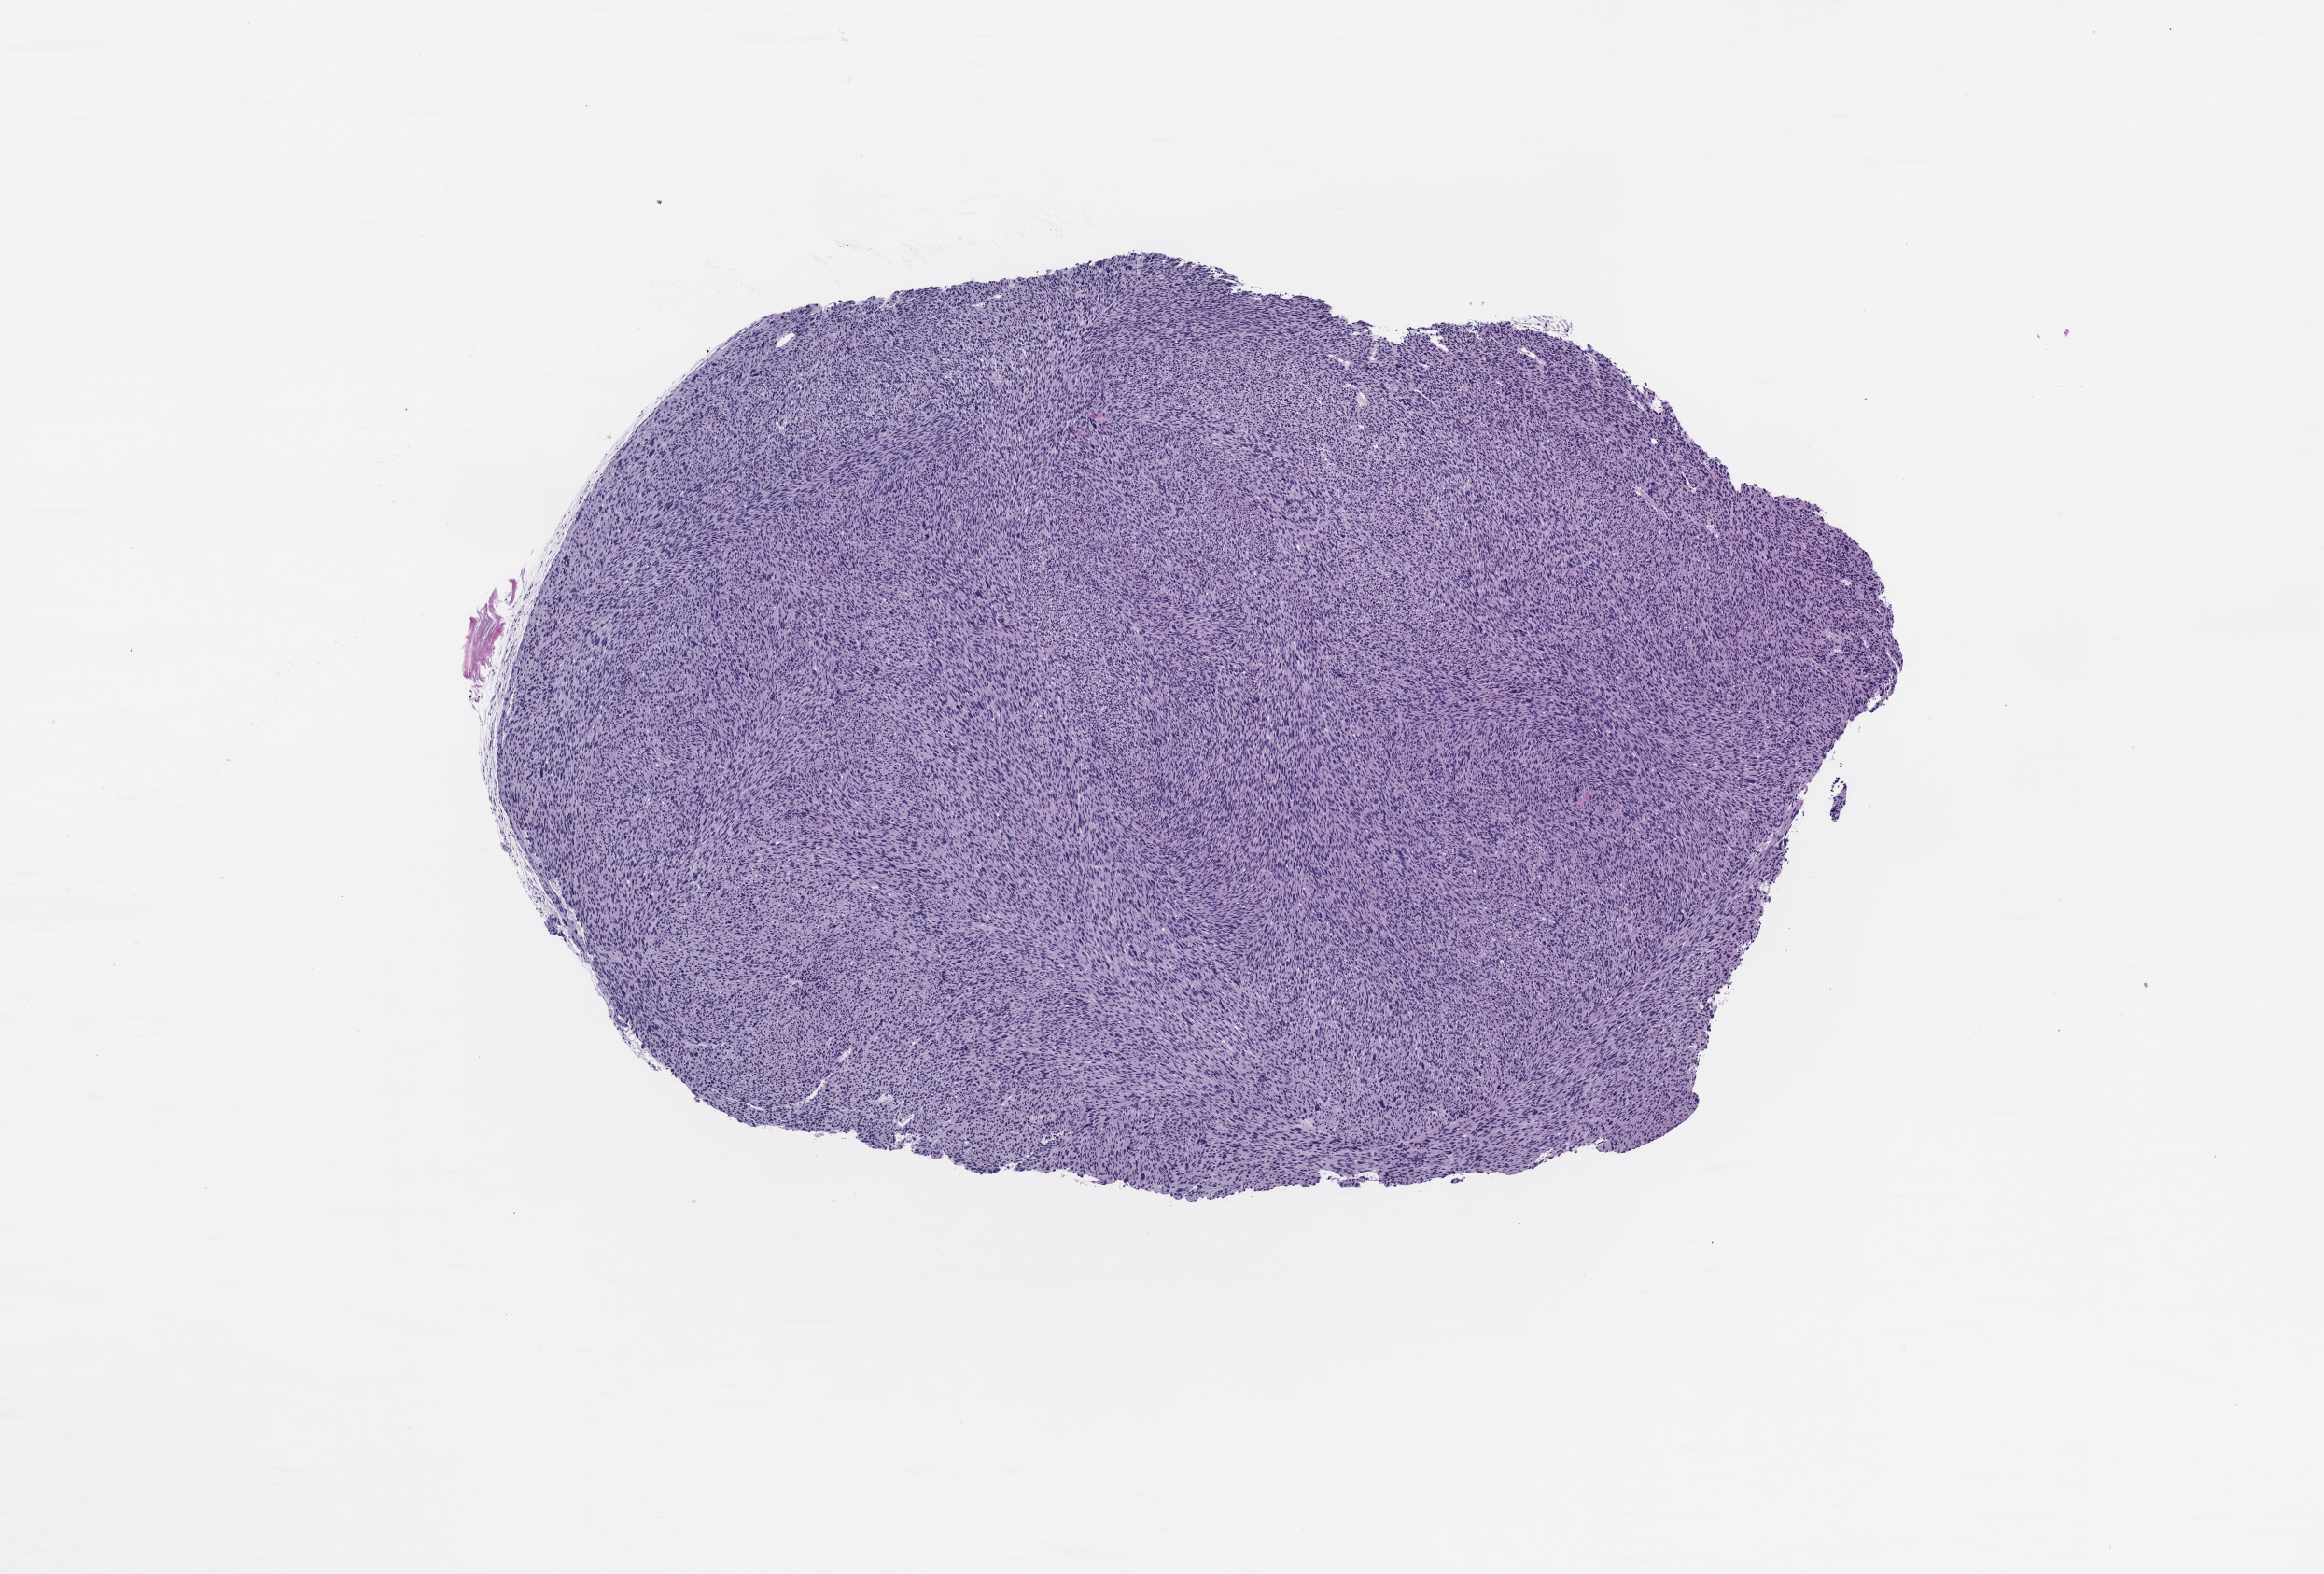
Whole-slide image, hematoxylin and eosin (H&E): patient-derived xenograft (human tumor grown in a mouse), passage 2, low-resolution overview of the scanned area, about 10.0 x 6.8 mm. FFPE section. Tumor site category: musculoskeletal.
Originating patient diagnosis: Leiomyosarcoma.